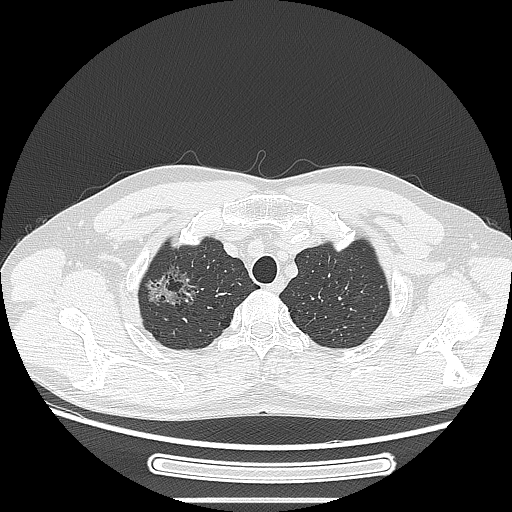
Chest CT, one axial slice; position 227 of 269 along the scan axis; reconstruction kernel LUNG; 120 kVp; lung window (W 1500 / L -600 HU); 1.25 mm slice thickness; 512 × 512 image matrix, field of view 382 × 382 mm. Patient: male, 53 years. From the clinical record (not read from this slice): clinical TNM (as recorded): T1c N0 M0; histopathological grade: G2.
Structures marked on this image (bounding box drawn by a radiologist):
- lung tumour (recorded histology: adenocarcinoma): bounding box [x1, y1, x2, y2] px = [138, 258, 200, 318]